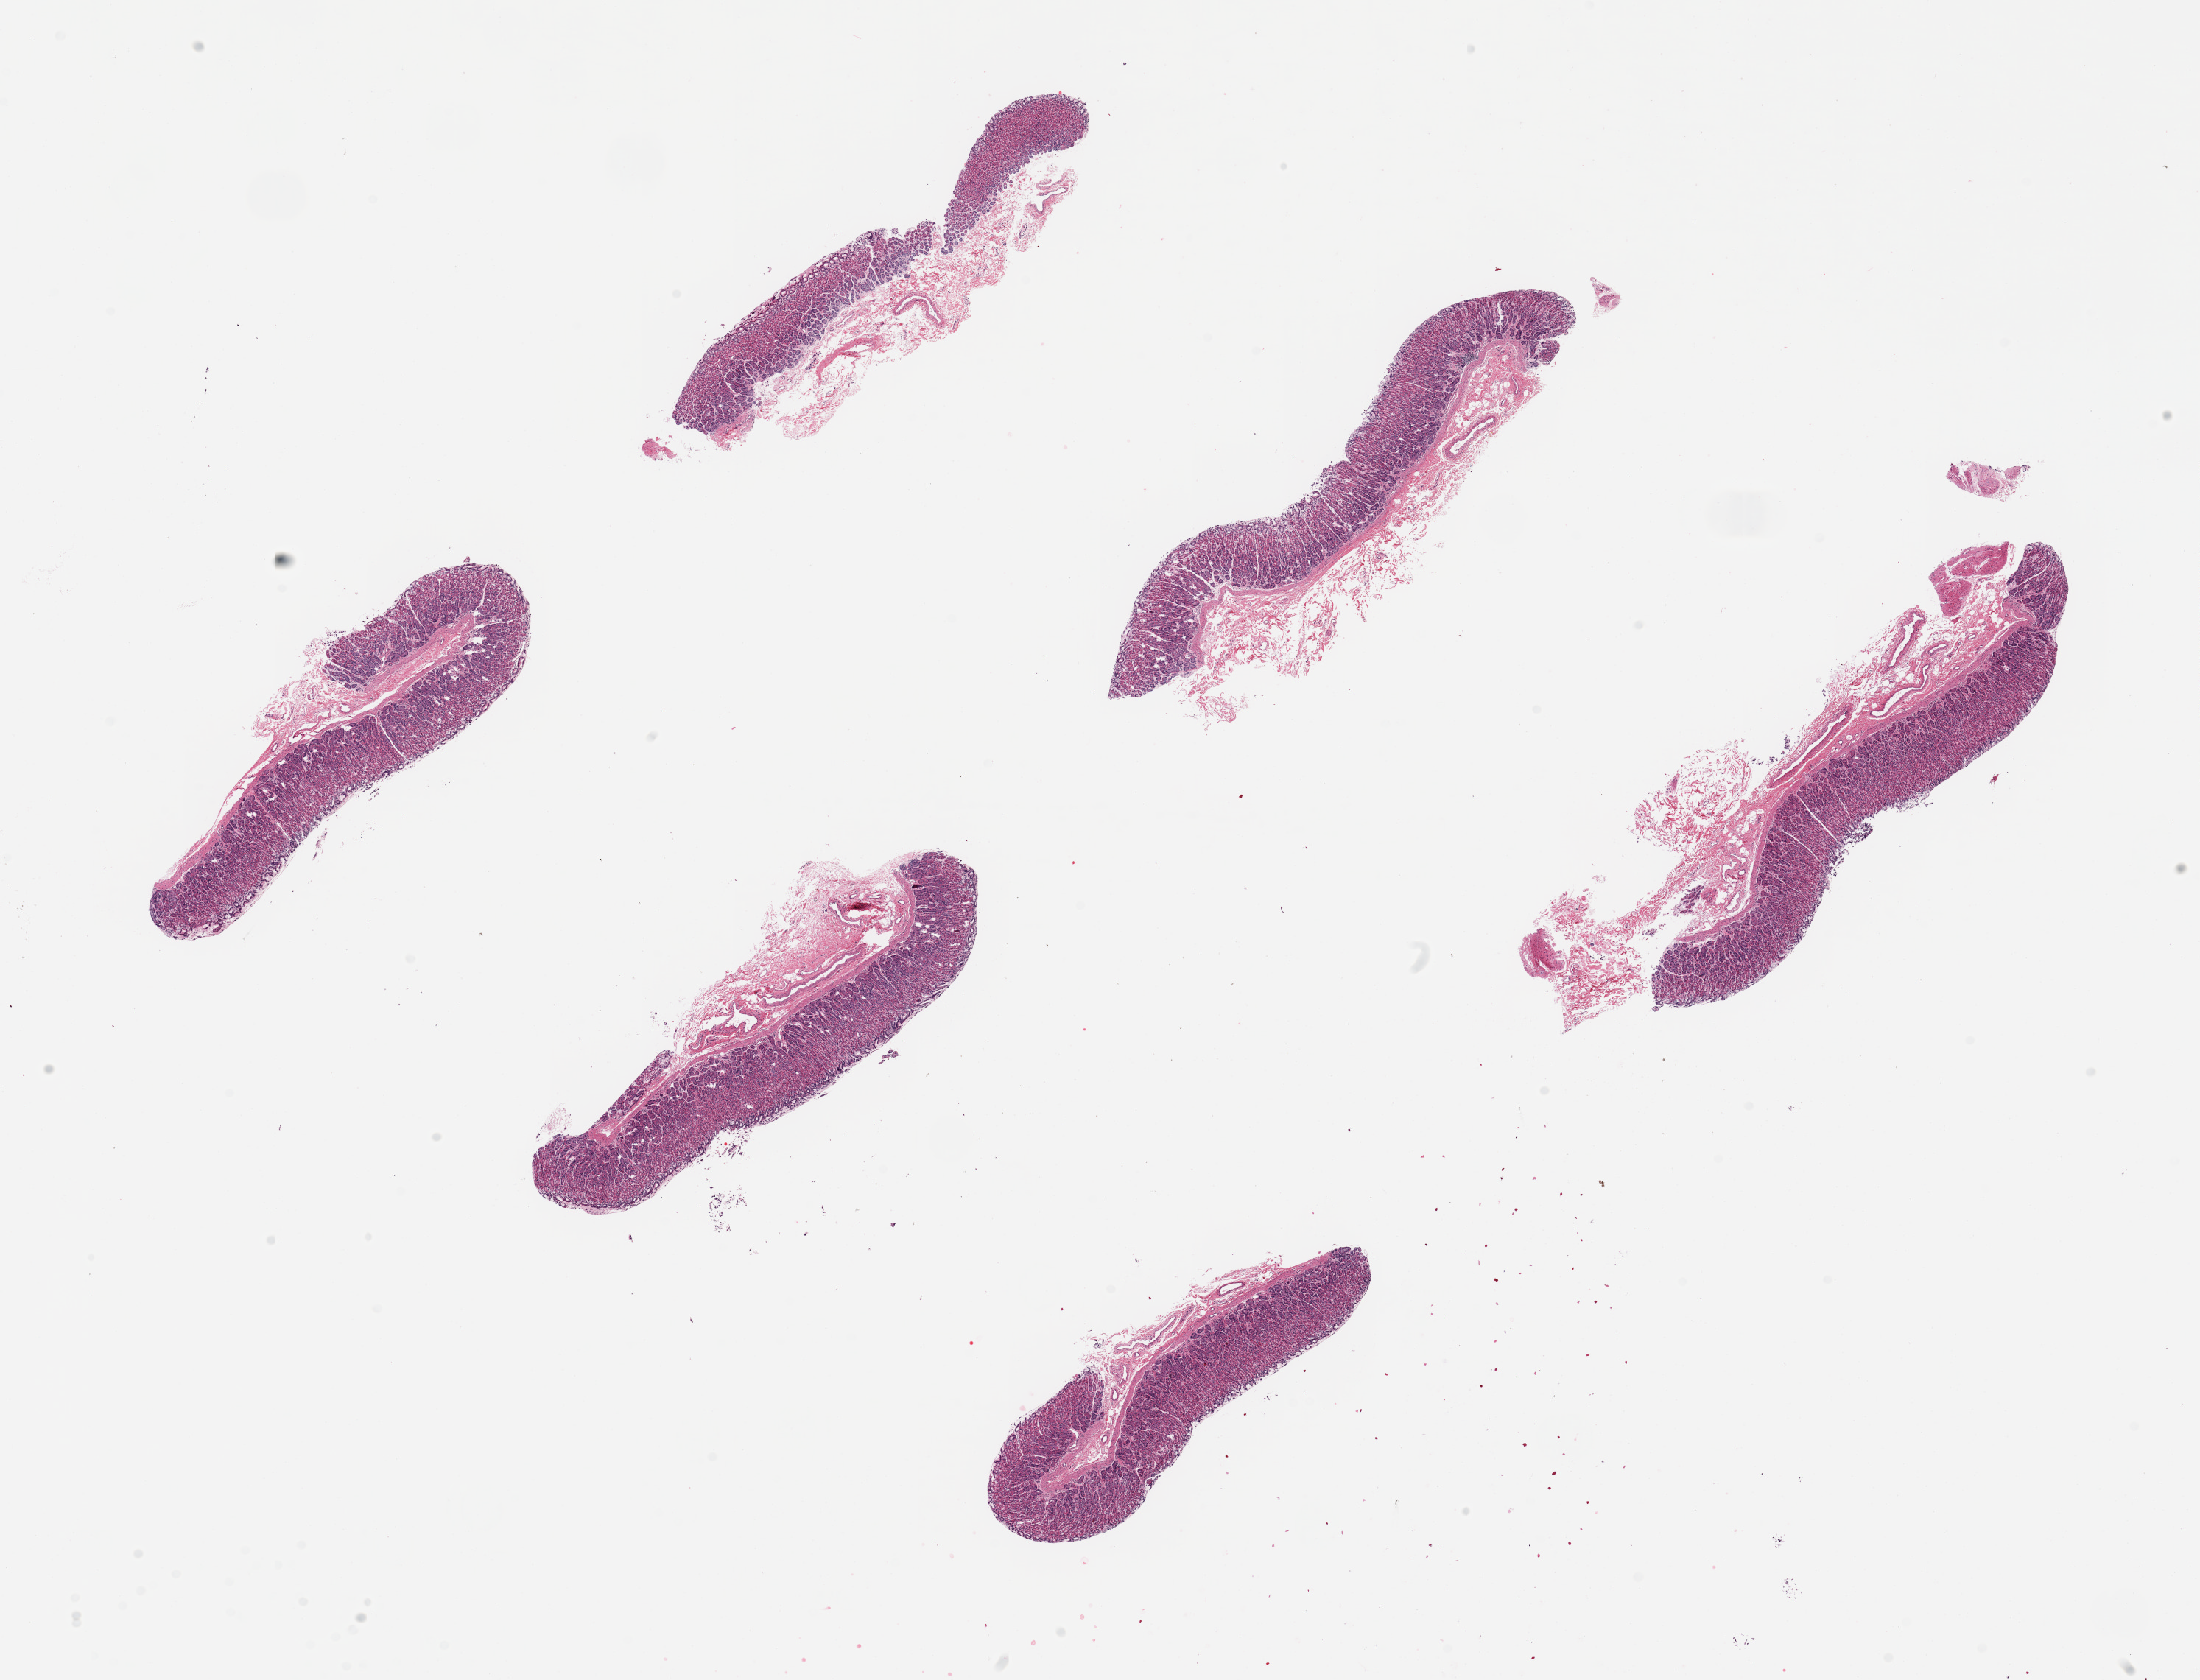
Whole-slide image, haematoxylin and eosin stain, brightfield — low-resolution overview of the scanned area, about 23.6 x 18.0 mm (acquisition: 20x scan), PAXgene-fixed, paraffin-embedded tissue, sampled site (target tissue): stomach, tissue donor sample. Male donor.
Reviewer comment on this tissue sample: 6 pieces up to 7x2 mm; good oxyntic mucosa on all, up to 0.8 mm; foveolar surface largely sloughed.